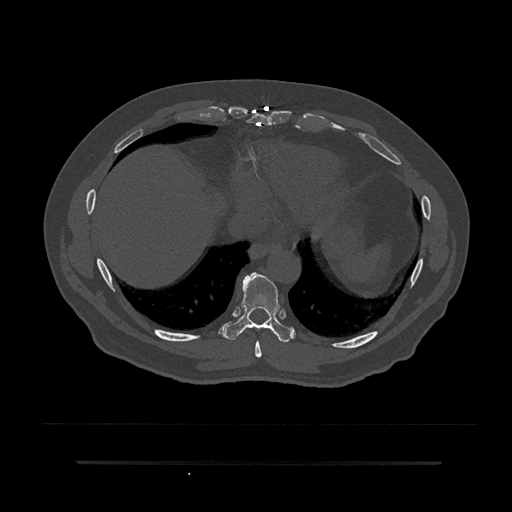
CT including the spine, one axial slice. Slice 387 of 797 in the series (ordered by position). Reconstruction kernel Br40s/3. 120 kVp. Bone window (W 1800 / L 400 HU). 512 × 512 image matrix, field of view 464 × 464 mm. Male patient, age 59 years. From the clinical record (not read from this slice): primary cancer: bile ducts; vertebrae with lytic lesions (as recorded): T10.
Outlined on this slice (semi-automatic segmentation, software-assisted and operator-edited):
- T8 vertebra: bounding box [x1, y1, x2, y2] px = [255, 340, 262, 357]
- T9 vertebra: [225, 272, 292, 342]